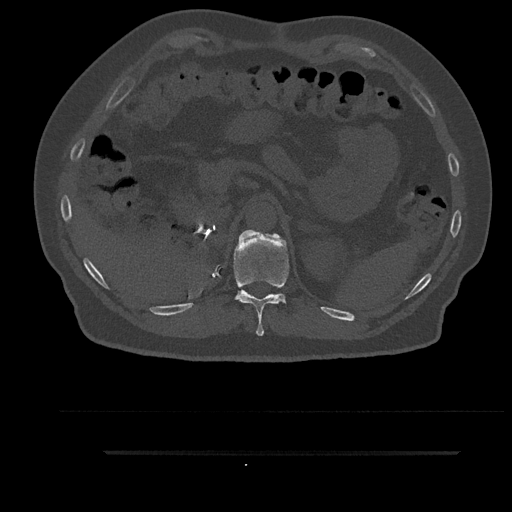
CT including the spine, one axial slice. Slice 295 of 797 in the series (ordered by position). Bone window (W 1800 / L 400 HU). 0.5 mm slice thickness. 512 × 512 image matrix. Male patient, age 63 years. Case-level facts recorded for this patient, not image findings: primary cancer: renal; vertebrae with lytic lesions (as recorded): T8.
Outlined on this slice (semi-automatic segmentation, software-assisted and operator-edited):
- T11 vertebra: bounding box <227,230,291,336> (left, top, right, bottom; pixels)